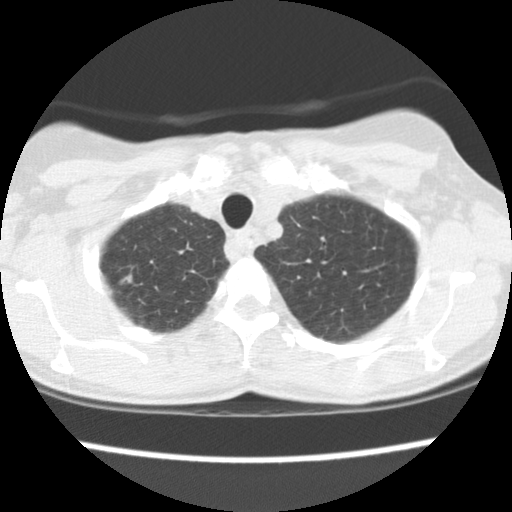
Low-dose screening chest CT, one axial slice; slice 129 of 148 in the series (ordered by position); reconstruction kernel STANDARD; 120 kVp; lung window (W 1500 / L -600 HU); 2.5 mm slice thickness; 512 × 512 image matrix, field of view 289 × 289 mm.
Structures marked on this image (expert manual segmentation):
- lesion 1 (tumor): box from (x=121, y=274) to (x=132, y=283) px